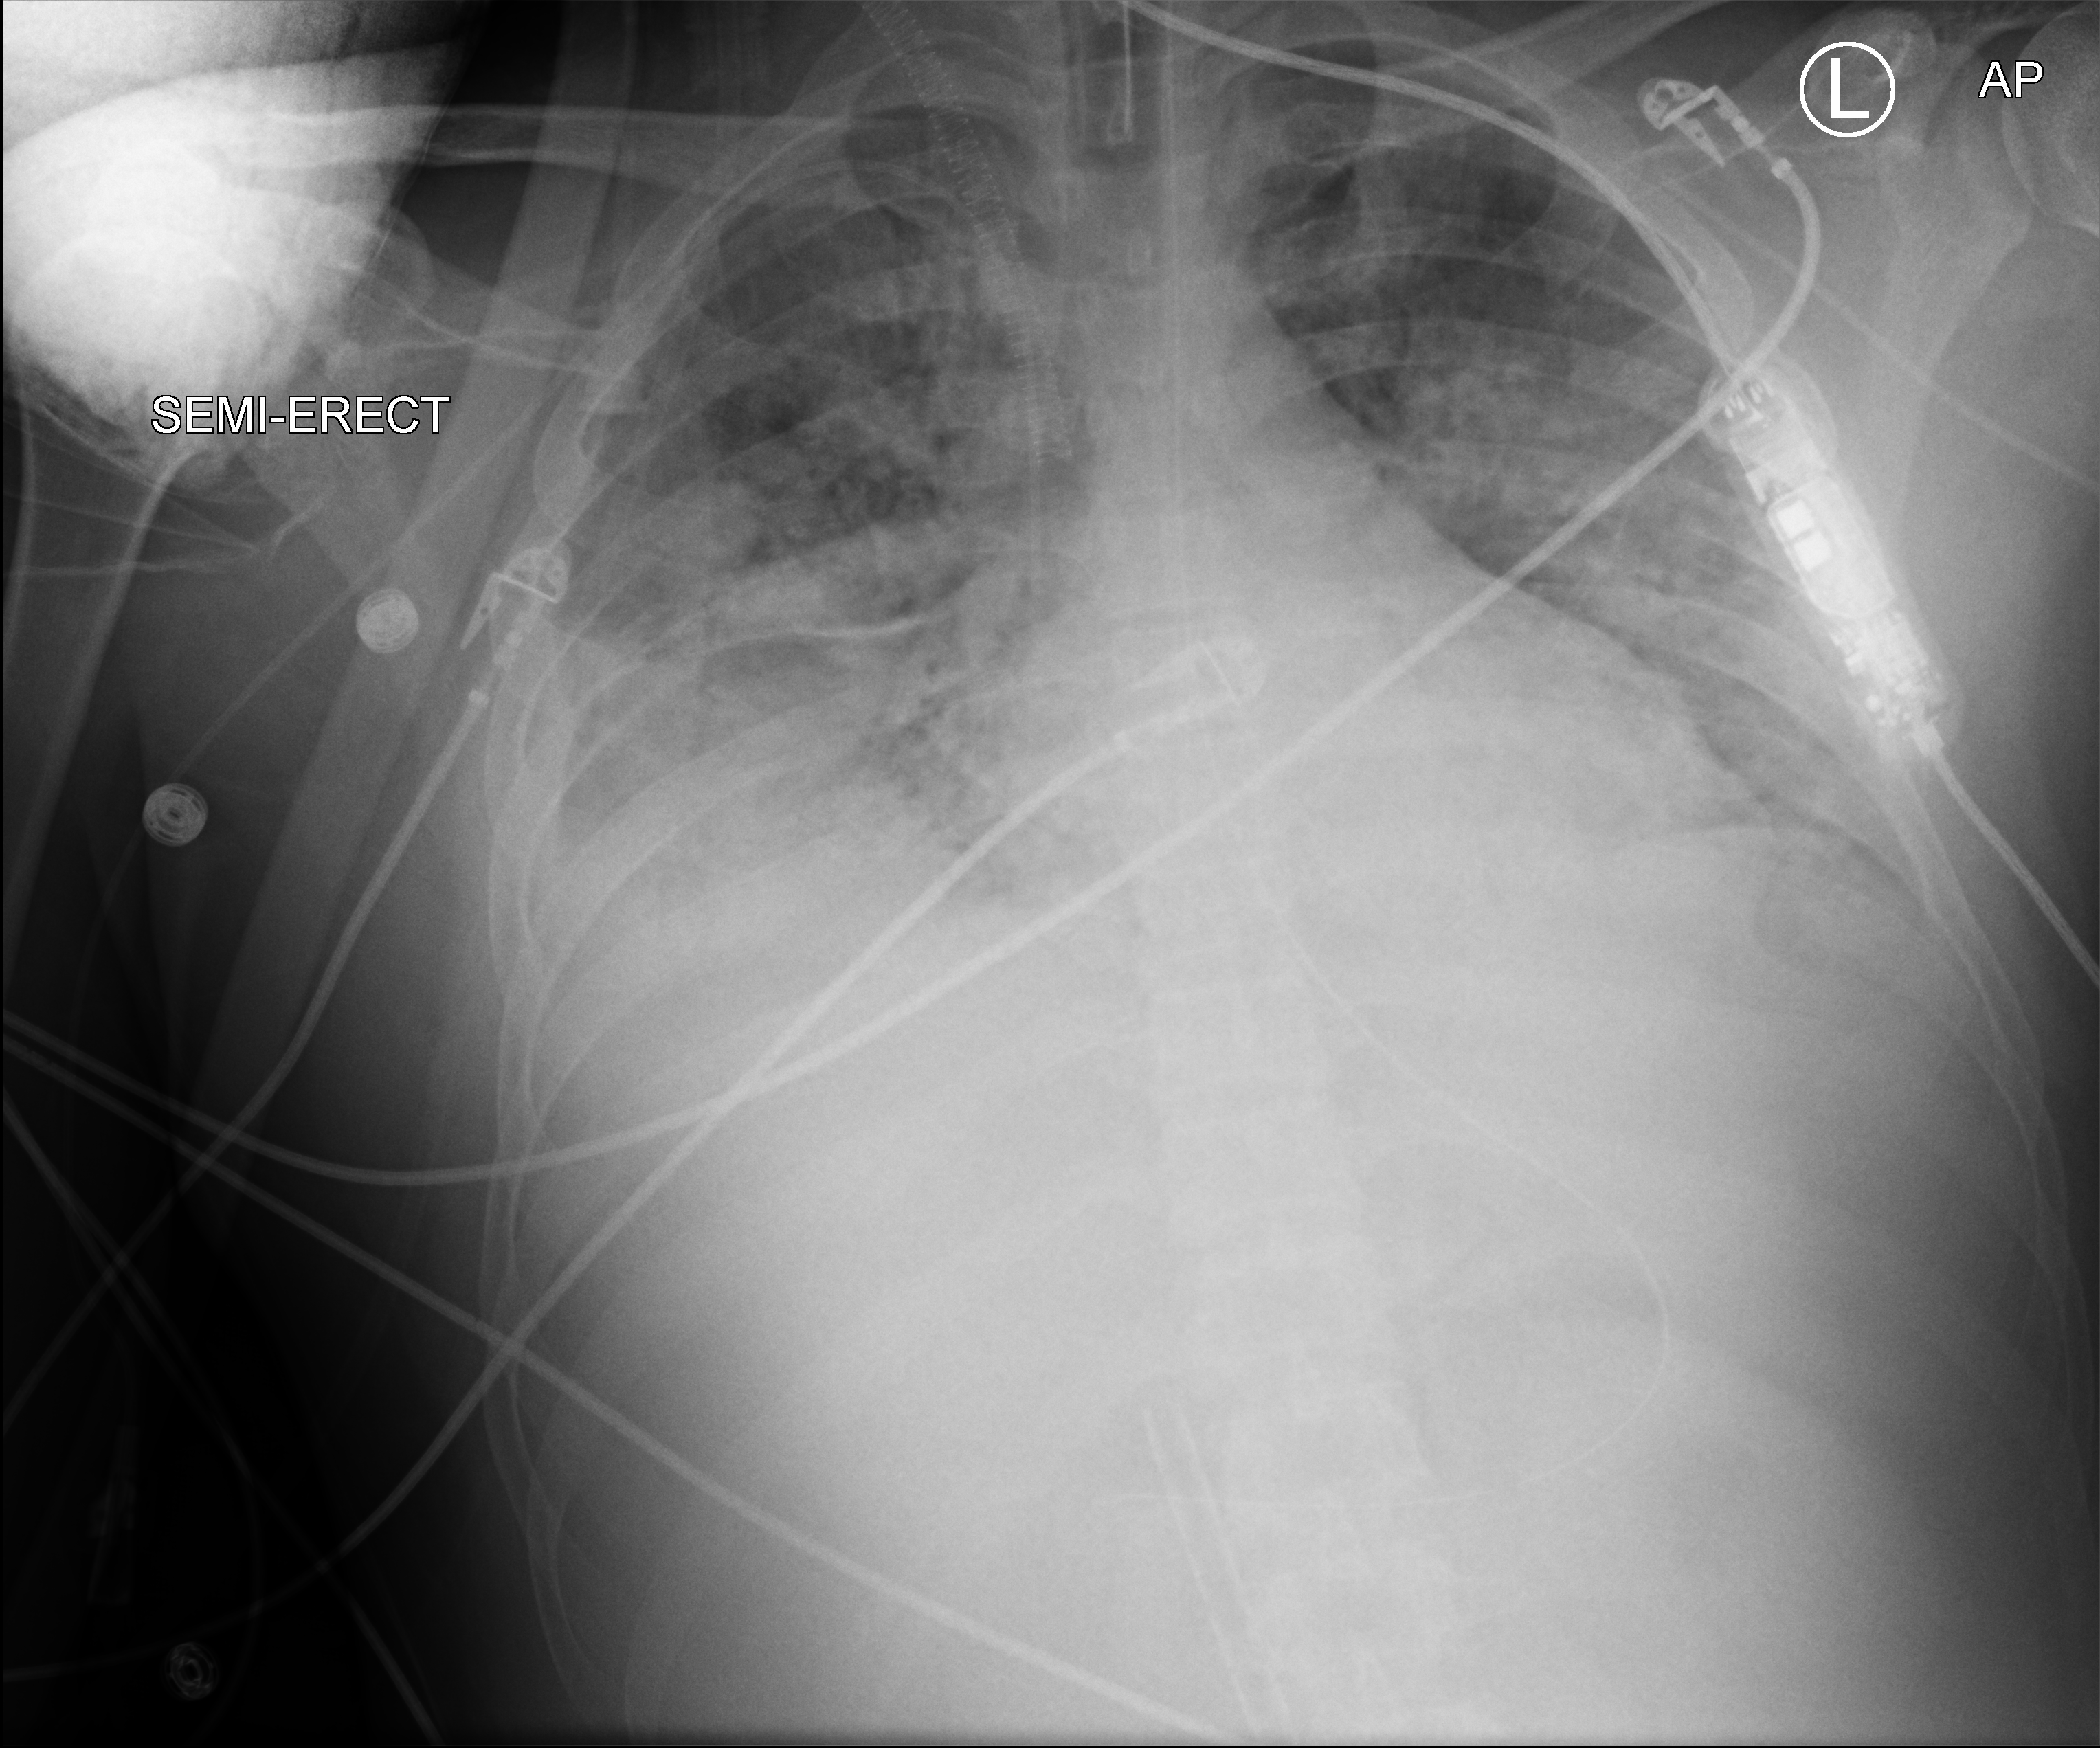
Portable chest radiograph, anteroposterior (AP) projection. Patient hospitalised with COVID-19, aged 18–59 years.
Hospital-stay facts (about this admission, not read from this image; timing relative to this image not recorded): admitted to intensive care during this hospital stay: yes; smoking status (admission record): never.